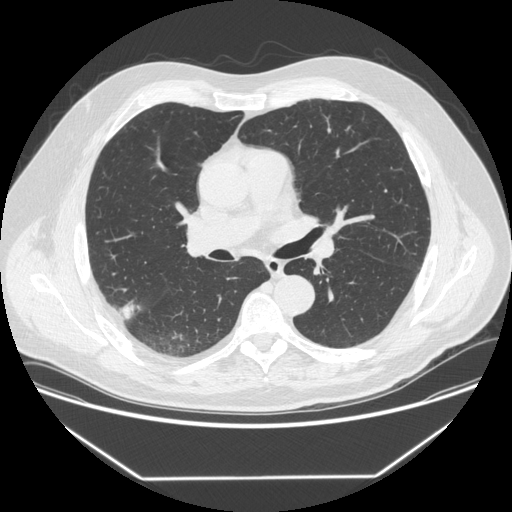
Axial slice from a low-dose chest CT screening exam. First (baseline) screen. Lung window (W 1500 / L -600 HU). 120 kVp. Male, age 64 years at enrolment.
Lesion marked by an expert reader, bounding box [x1, y1, x2, y2] px = [101, 298, 142, 329]. Screening reader's record for this exam (one nodule recorded; not confirmed to be the boxed lesion): non-calcified nodule or mass ≥4 mm, right upper lobe, 12 × 12 mm, smooth margins, soft tissue attenuation. Official screen result: positive, change unspecified: nodule(s) >= 4 mm or enlarging nodule(s), mass(es), or other non-specific abnormalities suspicious for lung cancer. Later outcome: lung cancer diagnosed 92 days after this screen — adenocarcinoma, NOS, right upper lobe, poorly differentiated (G3), stage IIIB (AJCC 6th edition), 15 mm at pathology.